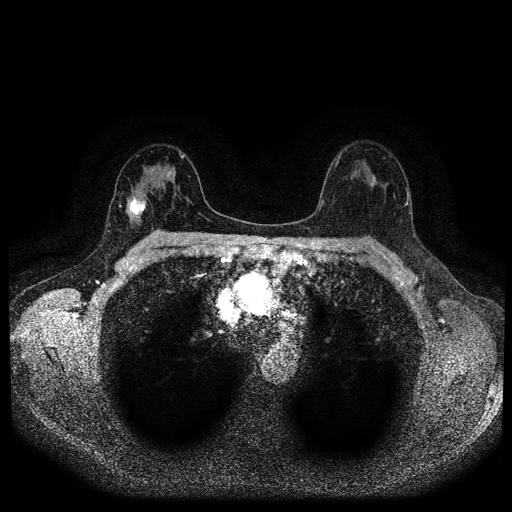
Breast MRI (dynamic contrast-enhanced, multi-phase), one axial slice. Slice 64 of 116 in the series (ordered by position). Dynamic contrast-enhanced series, time point 2 of 5 at this slice position (early post-contrast). 1.5 T. TE 2.7 ms, TR 5.4 ms. 2 mm slice thickness. 512 × 512 image matrix, field of view 330 × 330 mm. Female patient, age 42 years.
Outlined on this slice (semi-automatic segmentation, software-assisted and operator-edited):
- breast lesion (labelled 'tumour' in the annotation; benign lesions carry a separate 'benign' label): bounding box [x1, y1, x2, y2] px = [125, 193, 149, 221]